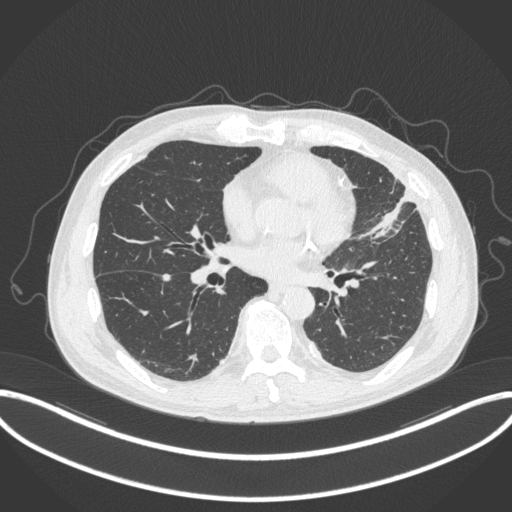
Chest CT, one axial slice. Slice 148 of 382 in the series (ordered by position). 120 kVp. Lung window (W 1500 / L -600 HU). 1 mm slice thickness. 512 × 512 image matrix, field of view 415 × 415 mm. Patient: male, 64 years. From the clinical record (not read from this slice): clinical TNM (as recorded): T4 N1 M0; histopathological grade: G3.
Outlined on this slice (bounding box drawn by a radiologist):
- lung tumour (recorded histology: adenocarcinoma): box from (x=362, y=189) to (x=417, y=241) px